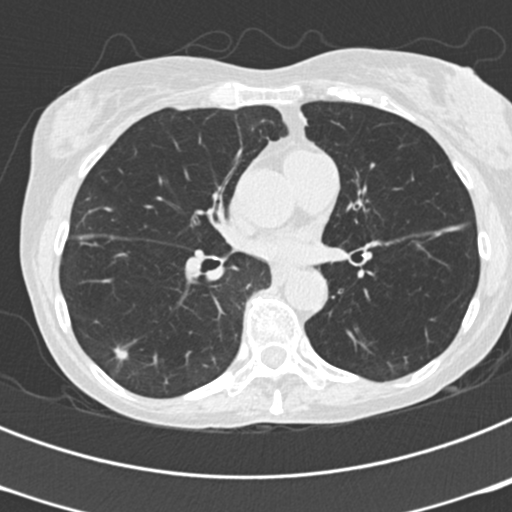
Low-dose screening chest CT, one axial slice; position 108 of 199 along the scan axis; lung window (W 1500 / L -600 HU); 2 mm slice thickness; 512 × 512 image matrix, field of view 290 × 290 mm.
Outlined on this slice (manually delineated by an expert):
- lesion 1 (tumor, lower lobe of right lung): bounding box <114,347,128,359> (left, top, right, bottom; pixels)